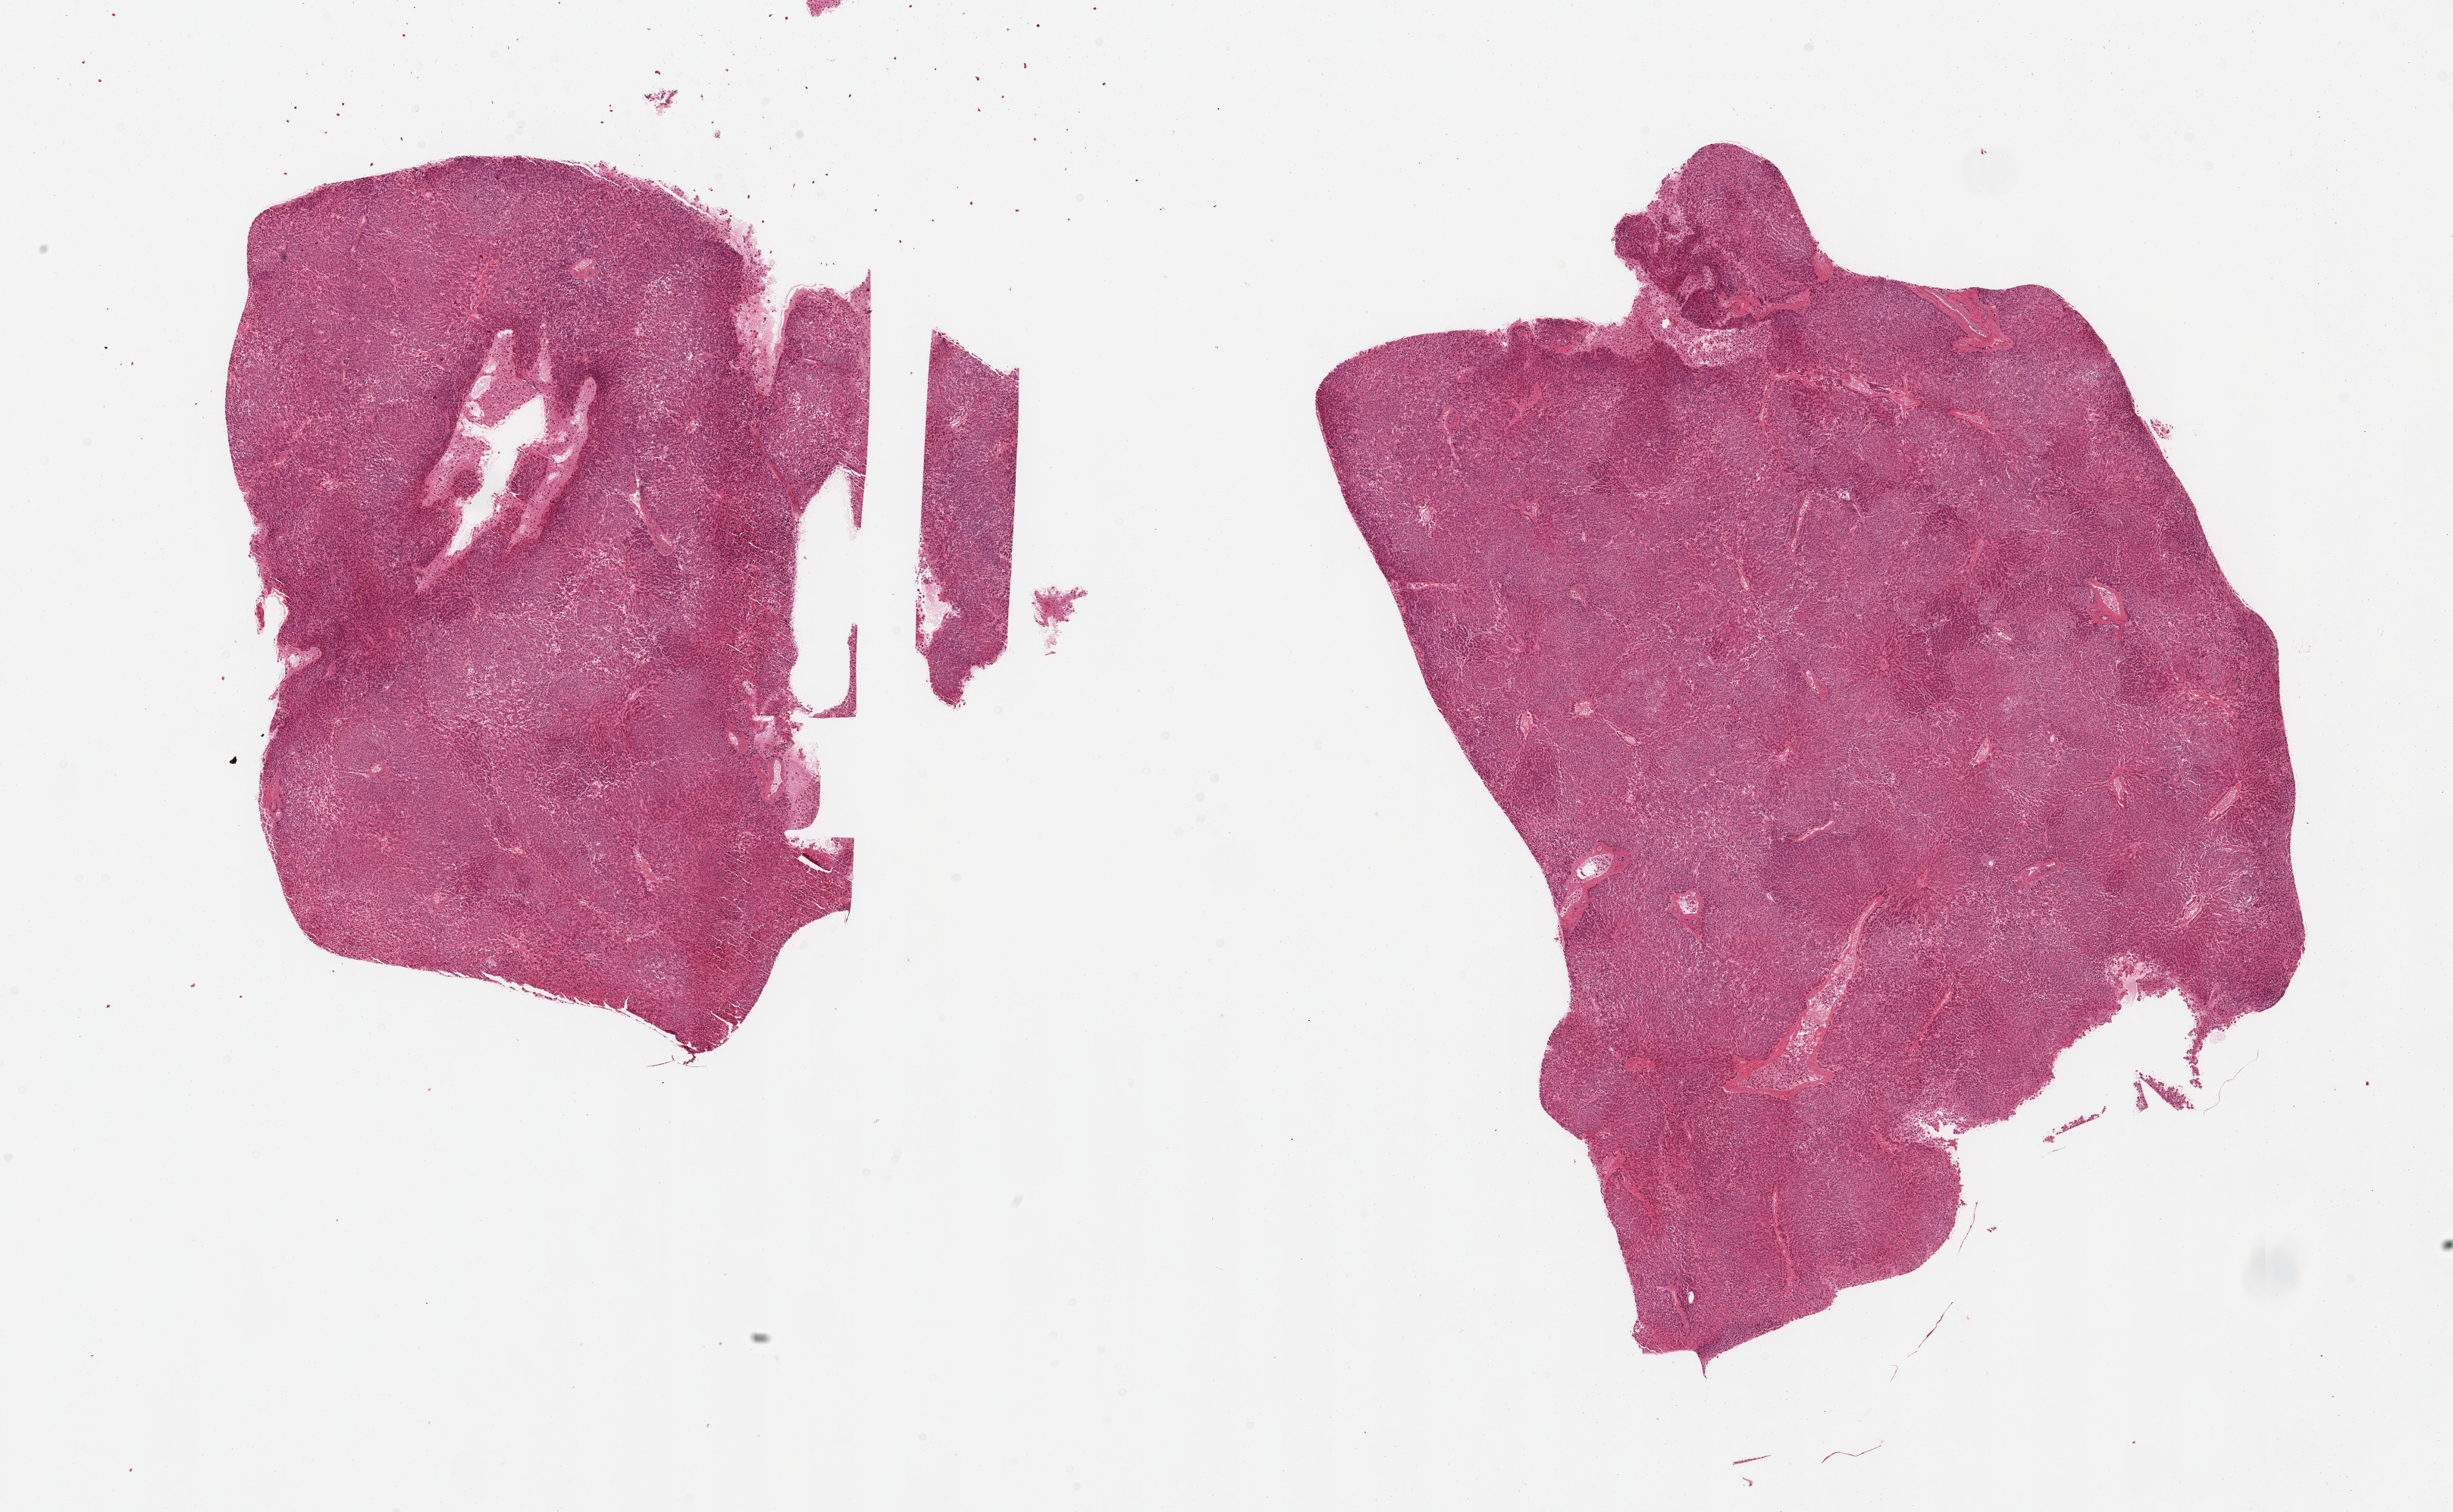
Whole-slide image, hematoxylin and eosin (H&E) stain, whole scanned area (about 25.6 x 15.8 mm, slide scanned at 20x) shown as a low-resolution overview; PAXgene-fixed, paraffin-embedded tissue; section of liver (target tissue); donor tissue sample. Donor: male.
* pathologist's review note for this sample: 2 pieces; <5% fat